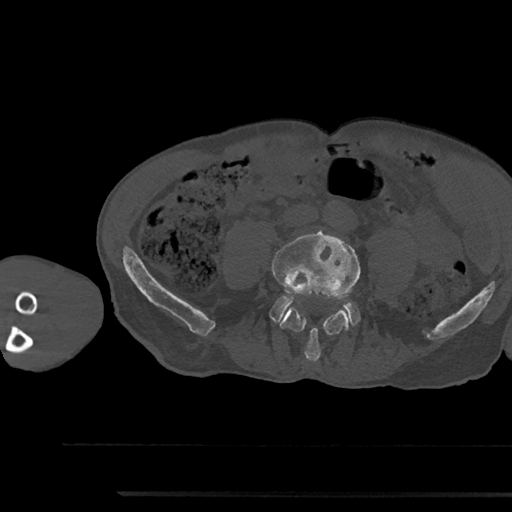
CT including the spine, one axial slice. Slice 389 of 797 in the series (ordered by position). 120 kVp. Bone window (W 1800 / L 400 HU). 512 × 512 image matrix, field of view 367 × 367 mm. Male patient, age 79 years. From the clinical record (not read from this slice): primary cancer: prostate.
Annotated regions visible in this slice (semi-automatically segmented with operator editing):
- L4 vertebra: bounding box (x1, y1, x2, y2) in pixels: (272, 231, 360, 362)
- L5 vertebra: (270, 296, 359, 325)